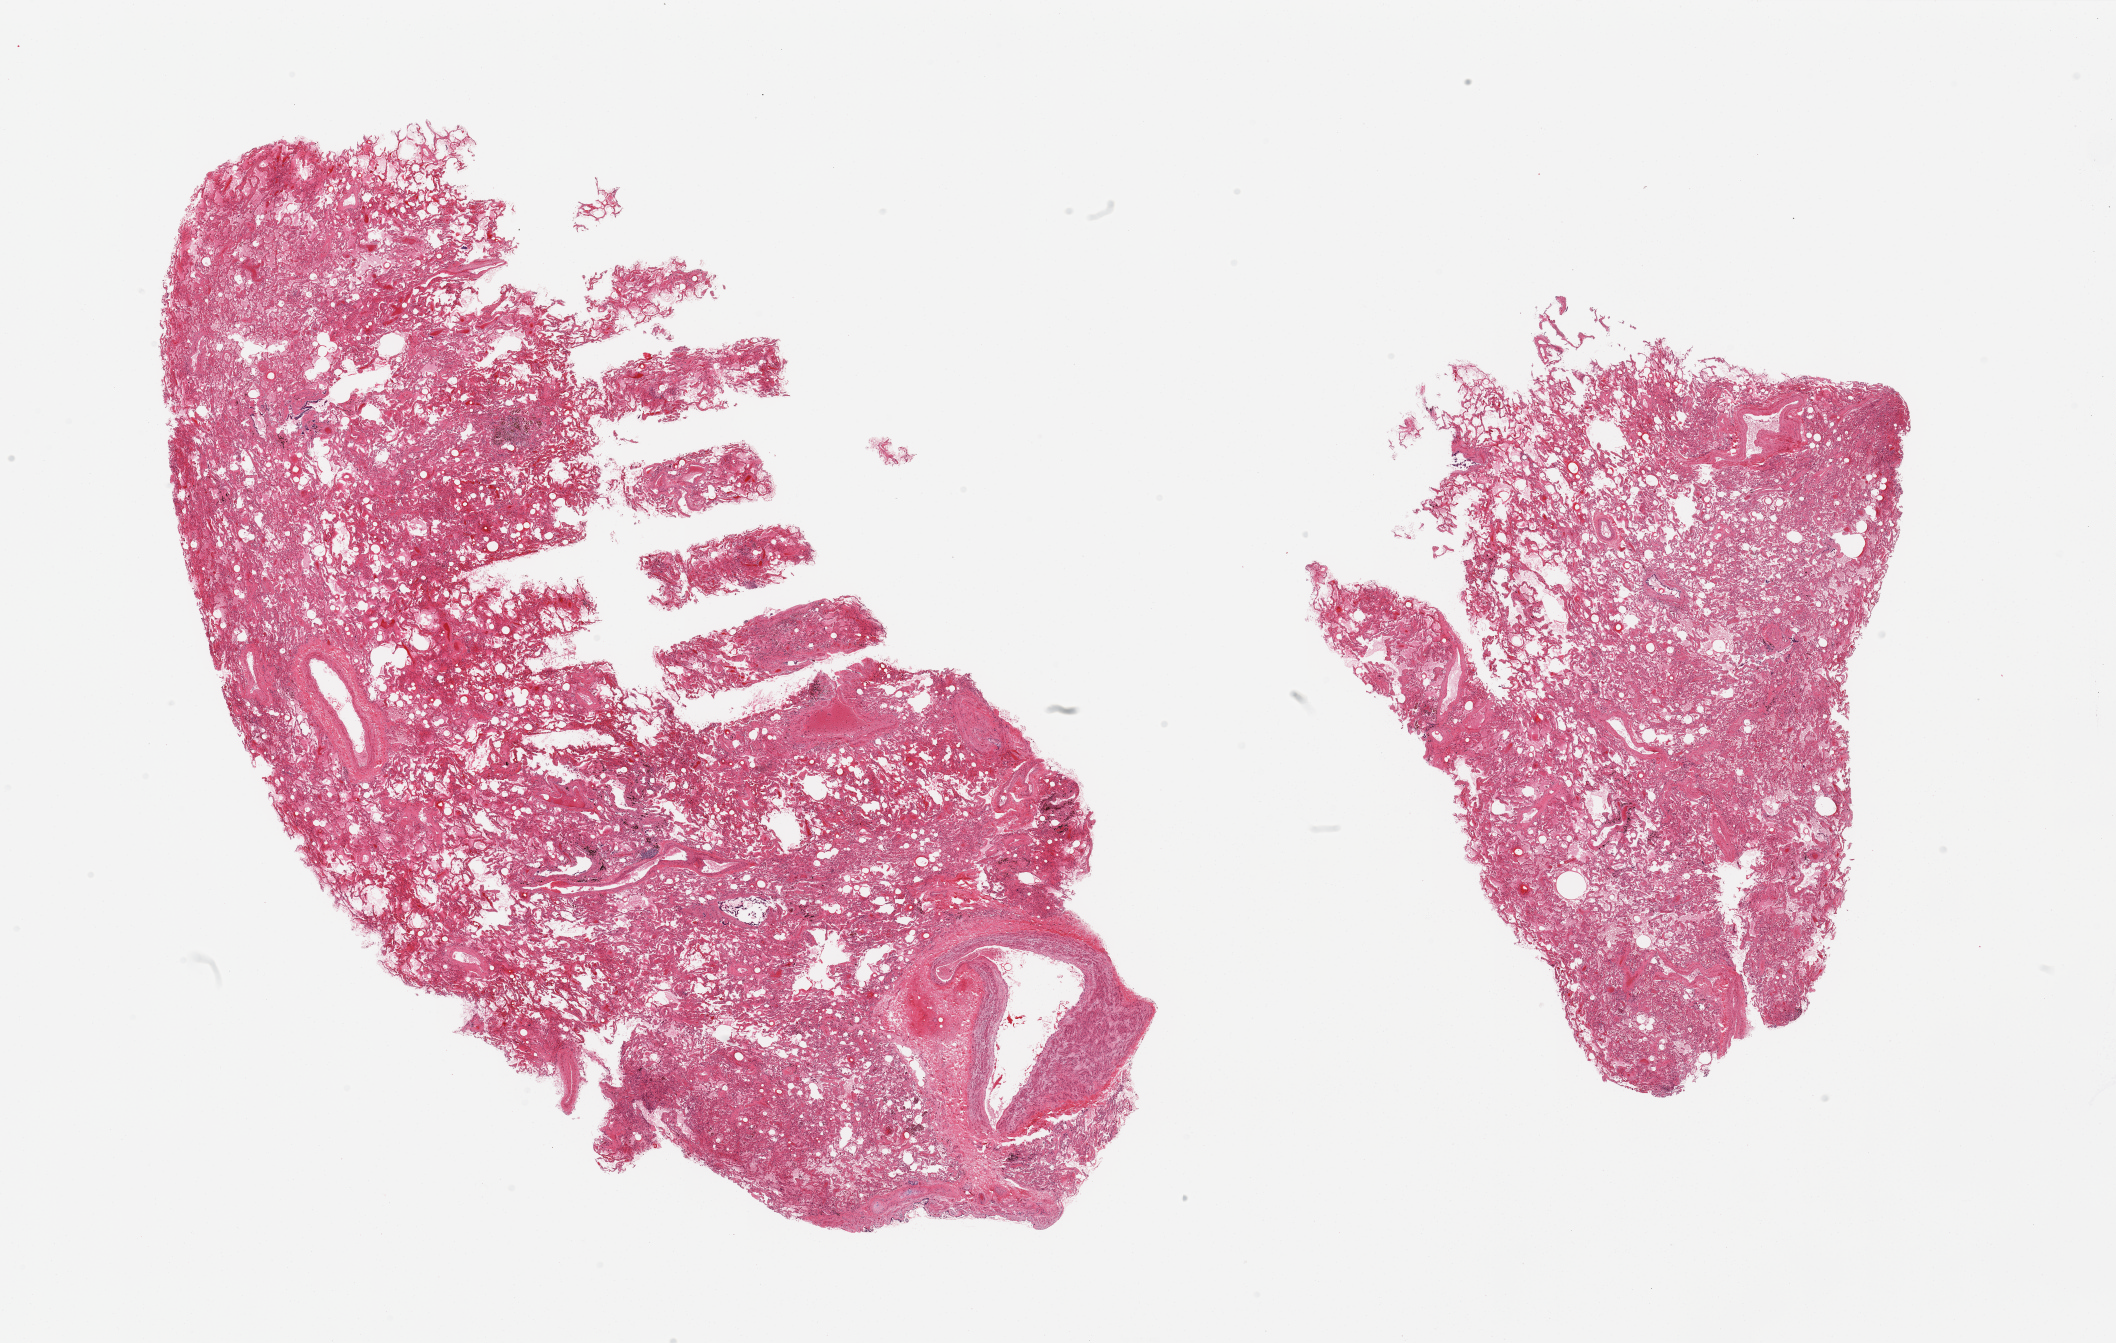
Whole-slide image, H&E stain — a low-resolution overview of the entire scanned area, about 33.5 x 21.2 mm. PAXgene-fixed paraffin-embedded (PFPE) section. Target tissue: lung. Tissue donor sample. Male donor.
Reviewer comment on this tissue sample: 2 pieces; congestion, edema, fibrosis, hemosiderin-laden macrophages, focus of cartilage, includes large vessels.